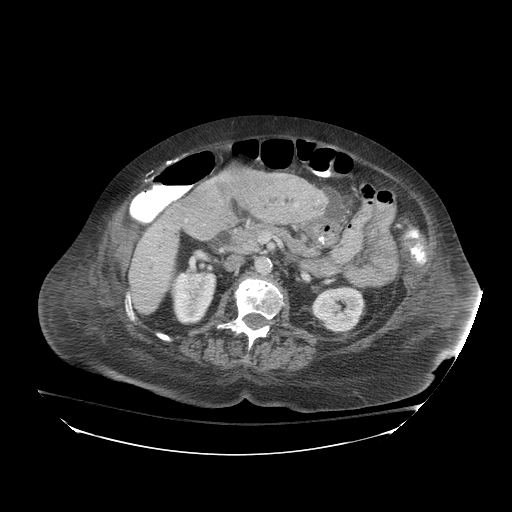
Contrast-enhanced abdominal CT (liver protocol), one axial slice. Slice 31 of 81 in the series (ordered by position). Reconstruction kernel STANDARD. 140 kVp. Soft-tissue window (W 400 / L 40 HU). 512 × 512 image matrix, field of view 500 × 500 mm. From the clinical record (not read from this slice): diagnosis: hepatocellular carcinoma (patient treated with transarterial chemoembolisation; whether this scan precedes or follows treatment is not stated here); TNM stage (as recorded): Stage-I; Child-Pugh class: B; tumour differentiation: well-moderately differentiated.
Annotated regions visible in this slice (semi-automatic segmentation, software-assisted and operator-edited):
- liver parenchyma outside the tumour (the mass and vessels are separate outlines, so this box may not span the whole liver): bounding box [x1, y1, x2, y2] px = [112, 202, 188, 314]
- mass: [212, 173, 257, 205]
- liver vessels: [127, 258, 156, 301]